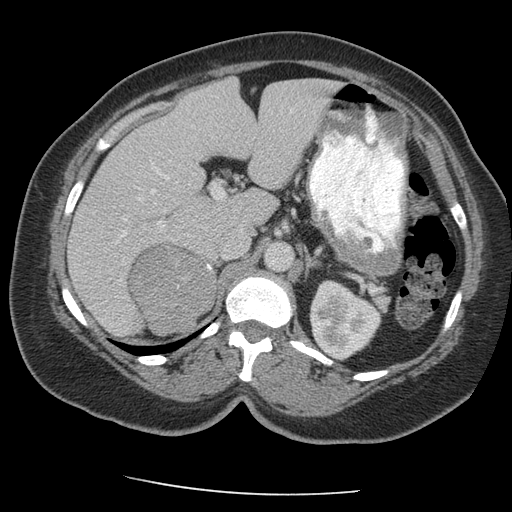
Contrast-enhanced abdominal CT, one axial slice; position 126 of 163 along the scan axis; intravenous contrast given; soft-tissue window (W 400 / L 40 HU); 2.5 mm slice thickness; 512 × 512 image matrix, field of view 360 × 360 mm. Patient: female, 70 years. Case-level facts recorded for this patient, not image findings: diagnosis: adrenocortical carcinoma; tumour side: right adrenal; tumour size at pathology: 9.5 cm; Ki-67 index: 5 %; stage (as recorded): 2.
Outlined on this slice (semi-automatic segmentation, software-assisted and operator-edited):
- mass: bounding box <132,248,213,333> (left, top, right, bottom; pixels)